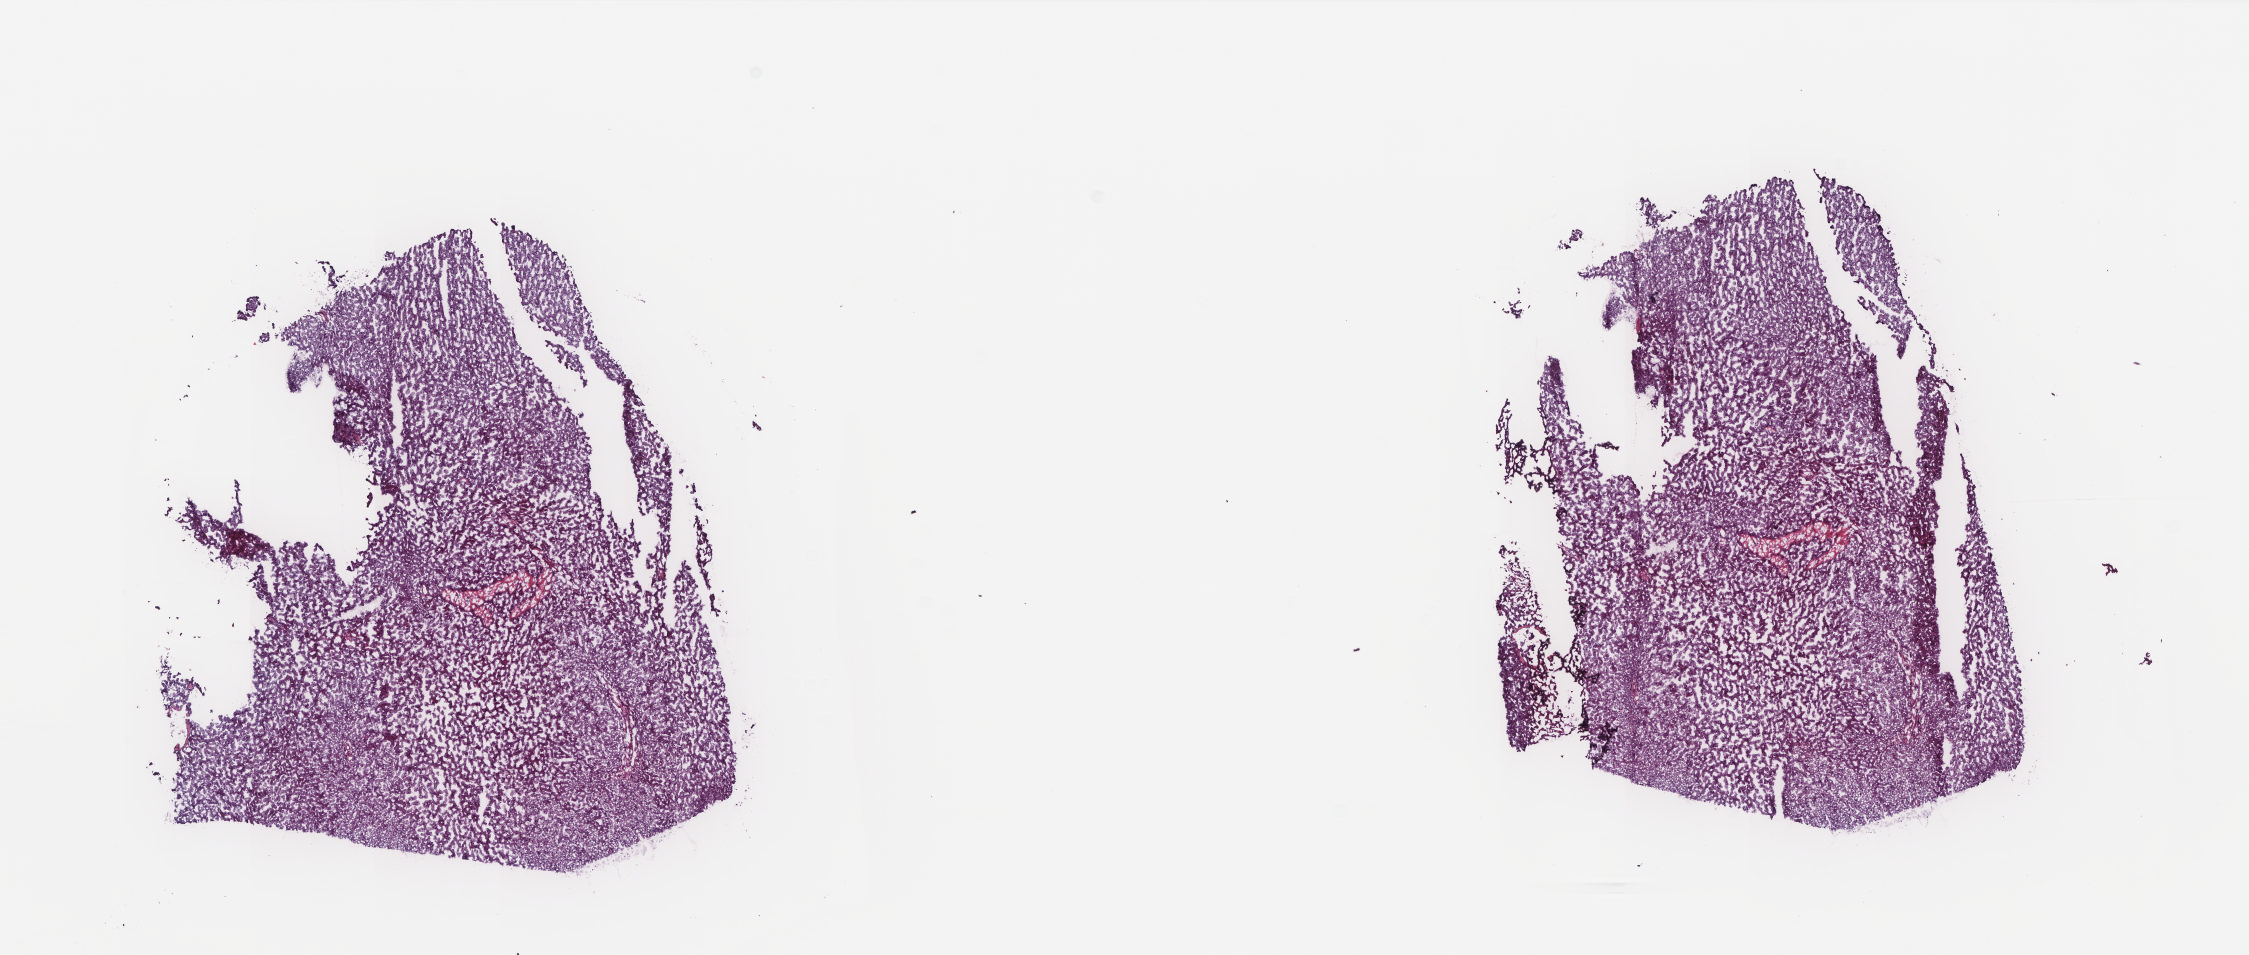
H&E-stained whole-slide image — whole scanned area (about 18.0 x 7.6 mm, slide scanned at 20x) shown as a low-resolution overview. Frozen section. Liver, solid tissue normal (non-tumour tissue) sample. Female patient; age at initial diagnosis 43 years. Slide review estimates, as recorded: tumour cells 0%, tumour nuclei 0%, normal cells 100%, stromal cells 0%, necrosis 0%. Inflammatory infiltration, as recorded: lymphocyte infiltration 1%, monocyte infiltration 0%, neutrophil infiltration 0%.
- this section: solid tissue normal (non-tumour) sample from the same patient
- patient diagnosis: Hepatocellular carcinoma, NOS